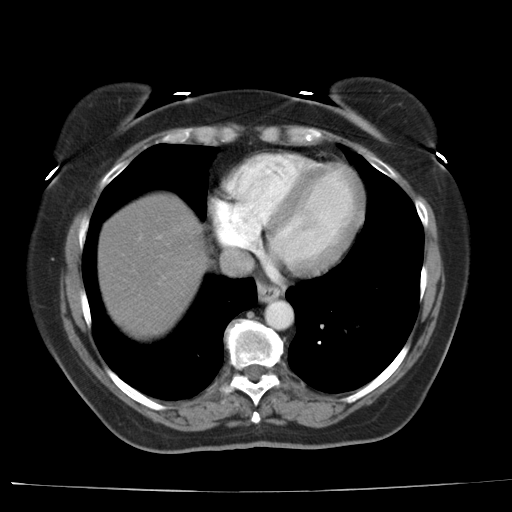
Contrast-enhanced abdominal CT, one axial slice; slice 35 of 44 in the series (ordered by position); reconstruction kernel AA-1; 140 kVp; intravenous contrast given; soft-tissue window (W 400 / L 40 HU); 5 mm slice thickness; 512 × 512 image matrix, field of view 373 × 373 mm. Female patient. From the clinical record (not read from this slice): diagnosis: colorectal cancer liver metastases, imaged before liver resection; multiple liver metastases: yes.
Structures marked on this image (expert manual segmentation):
- liver: bounding box [x1, y1, x2, y2] px = [97, 194, 209, 341]
- planned liver remnant (the part of the liver to remain after resection): [136, 194, 207, 255]